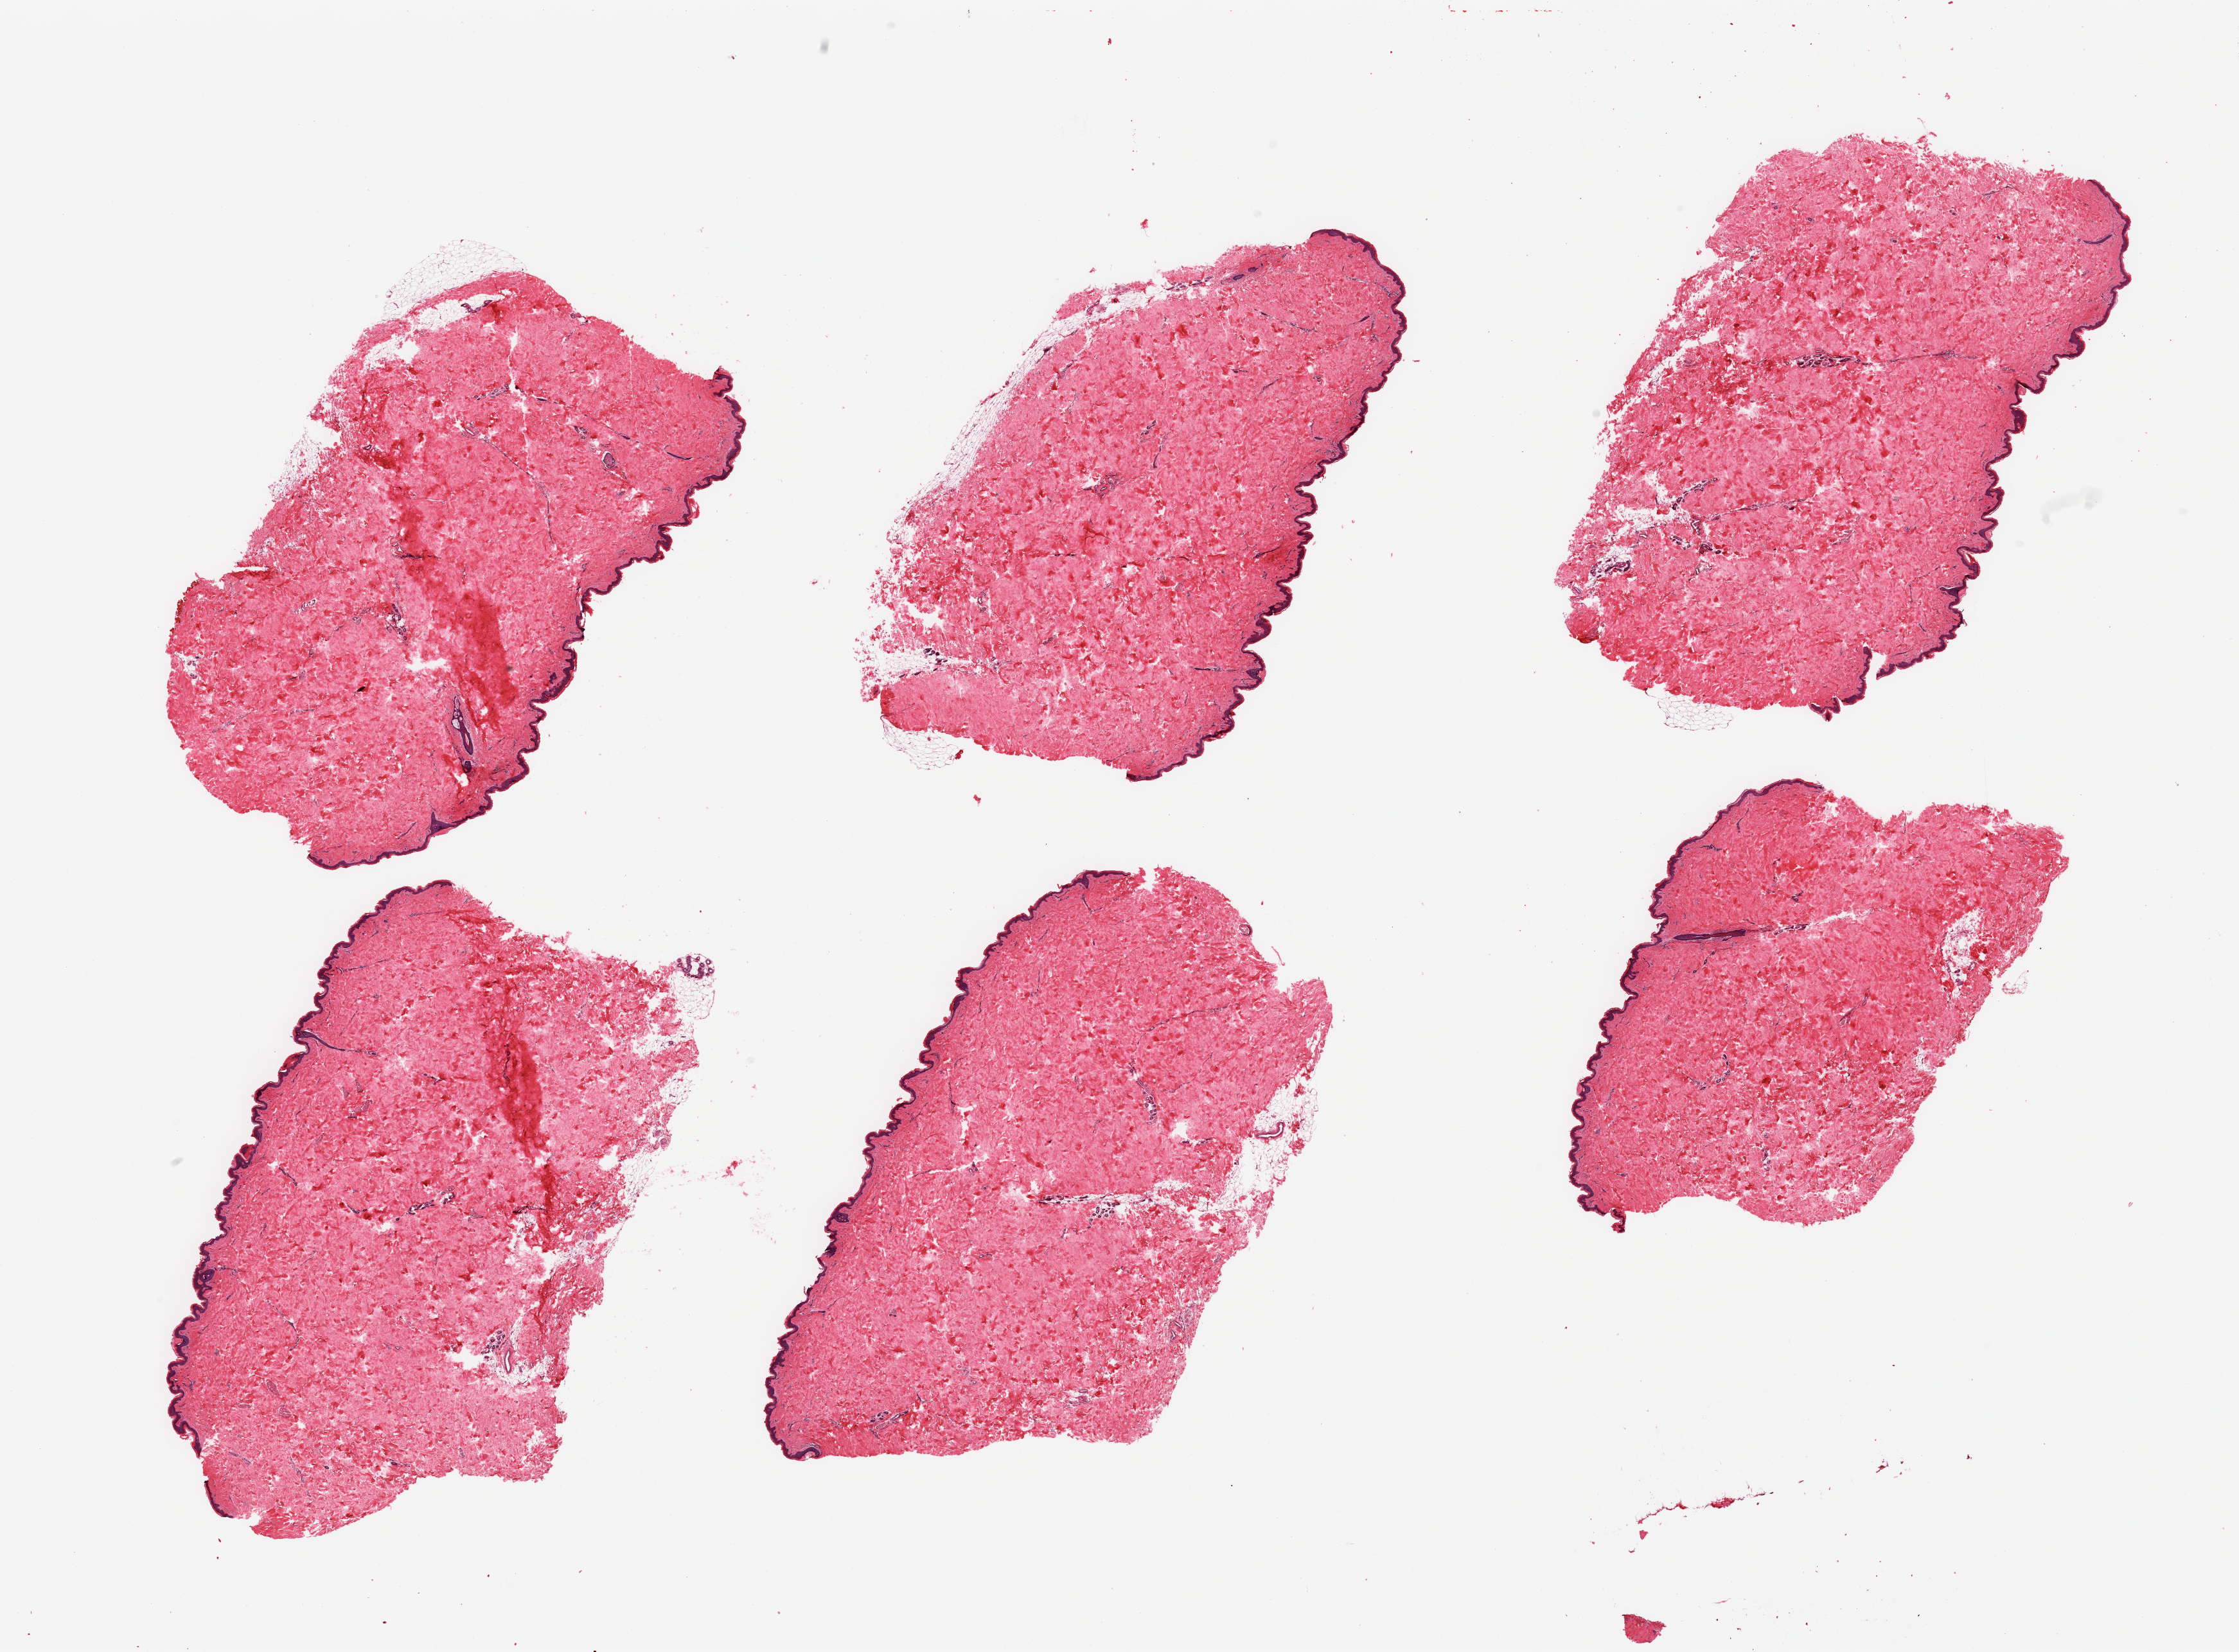
Digitized haematoxylin and eosin-stained section, whole scanned area (about 27.6 x 20.3 mm) shown as a low-resolution overview; PAXgene-fixed, paraffin-embedded tissue; section of skin of suprapubic region (target tissue); donor tissue sample. Donor: female.
• review note (as recorded): 6 pieces; well trimmed; minimal dermal fat